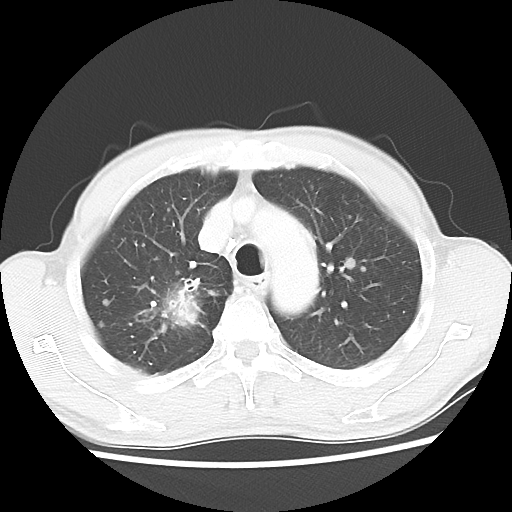
Chest CT, one axial slice; slice 40 of 52 in the series (ordered by position); reconstruction kernel LUNG; 100 kVp; lung window (W 1500 / L -600 HU); 5 mm slice thickness; 512 × 512 image matrix. Male patient, age 66 years. Case-level facts recorded for this patient, not image findings: clinical TNM (as recorded): T2 N0 M1a.
Annotated regions visible in this slice (bounding box drawn by a radiologist):
- lung tumour (recorded histology: adenocarcinoma): bounding box (x1, y1, x2, y2) in pixels: (133, 272, 217, 342)